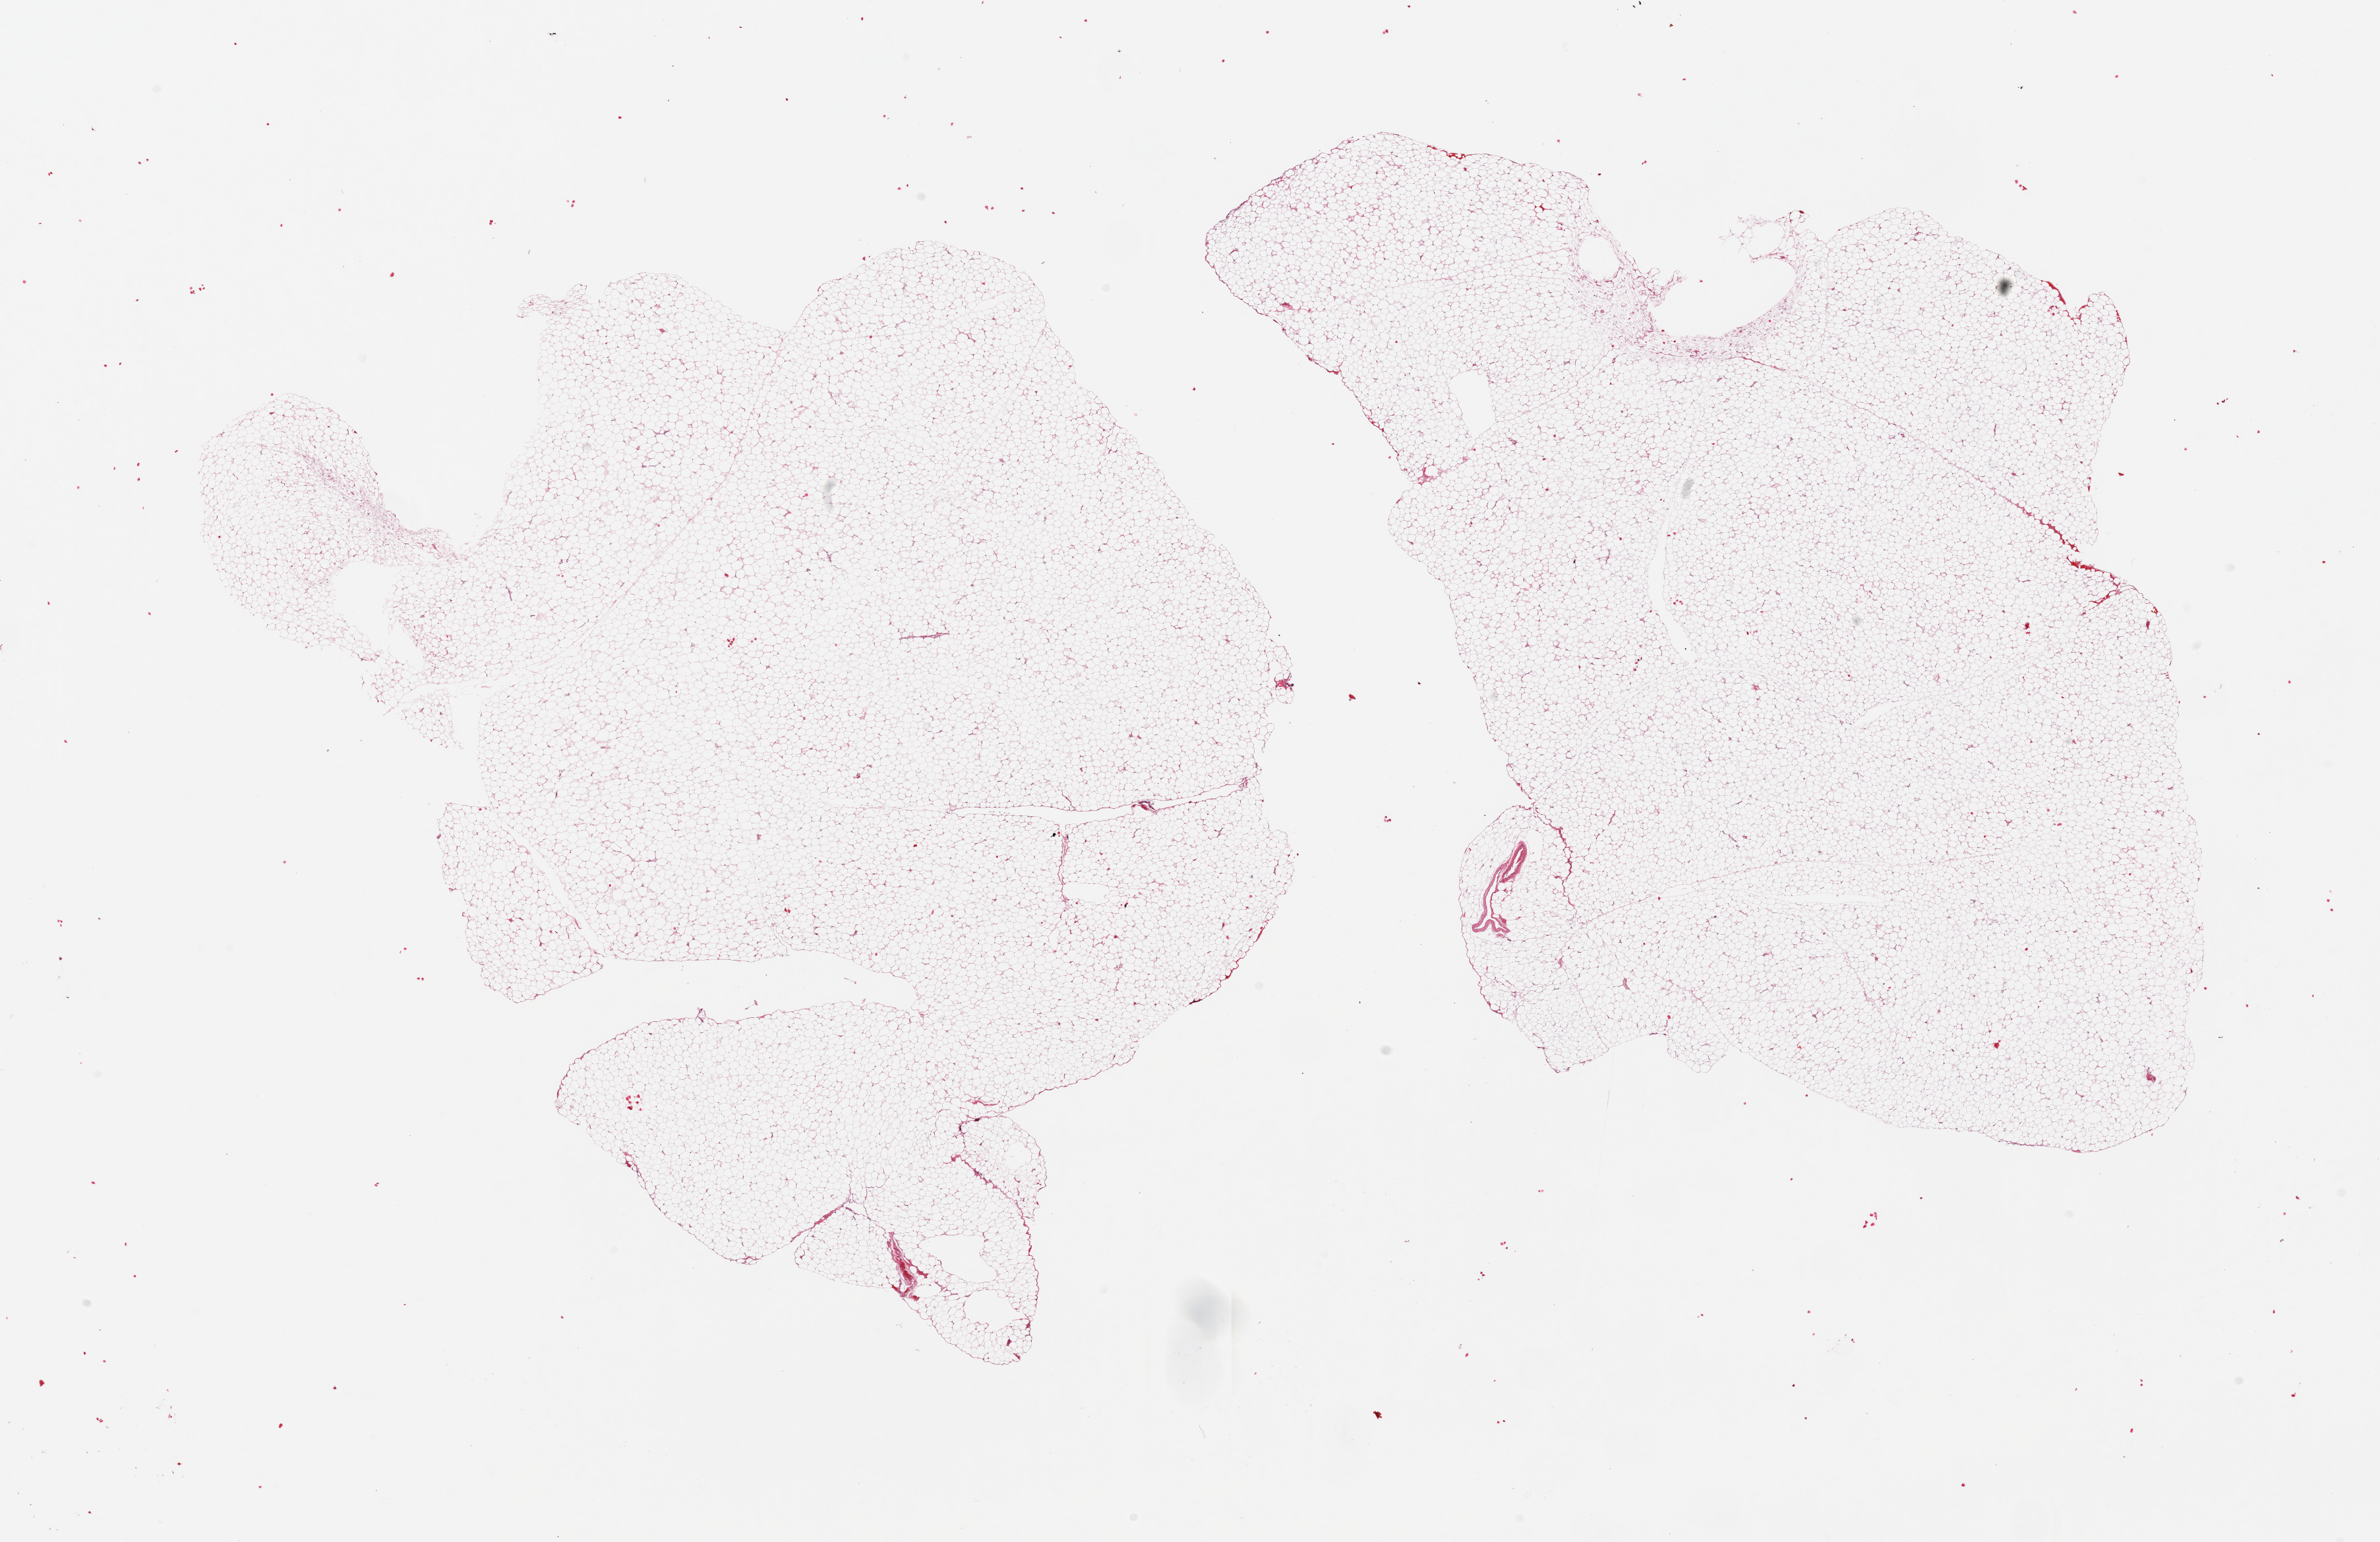
Digitized H&E-stained section, brightfield, whole scanned area (about 28.5 x 18.5 mm, from a 20x scan) shown as a low-resolution overview. PAXgene-fixed paraffin-embedded (PFPE) section. Target tissue: omentum. Donor tissue sample. Male donor.
Pathologist's review note for this sample: 2 pieces, trace fascia.